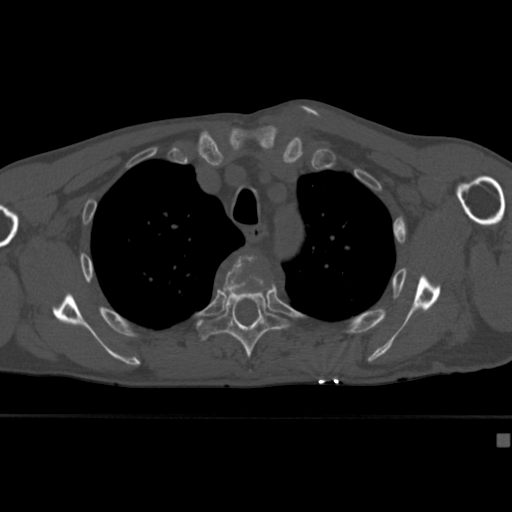
CT including the spine, one axial slice; slice 313 of 430 in the series (ordered by position); 120 kVp; bone window (W 1800 / L 400 HU); 512 × 512 image matrix. Patient: male, 64 years. Case-level facts recorded for this patient, not image findings: primary cancer: uterus; vertebrae with lytic lesions (as recorded): T1, T4, T5, T7, L5.
Outlined on this slice (semi-automatic segmentation, software-assisted and operator-edited):
- T4 vertebra: box from (x=223, y=255) to (x=274, y=298) px
- T5 vertebra: (x=197, y=290)–(x=290, y=372)